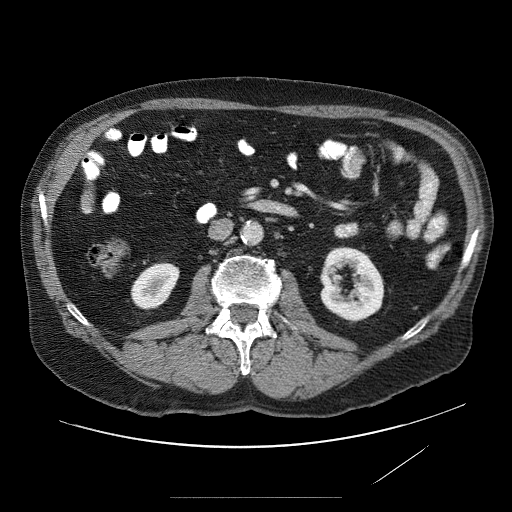
Contrast-enhanced abdominal CT (liver protocol), one axial slice; position 4 of 89 along the scan axis; reconstruction kernel STANDARD; 120 kVp; soft-tissue window (W 400 / L 40 HU); 512 × 512 image matrix, field of view 420 × 420 mm. From the clinical record (not read from this slice): diagnosis: hepatocellular carcinoma (patient treated with transarterial chemoembolisation; whether this scan precedes or follows treatment is not stated here); TNM stage (as recorded): Stage-IVA; Child-Pugh class: A; tumour nodularity: multinodular.
Annotated regions visible in this slice (semi-automatically segmented with operator editing):
- liver parenchyma outside the tumour (the mass and vessels are separate outlines, so this box may not span the whole liver): bounding box <78,160,104,222> (left, top, right, bottom; pixels)
- liver vessels: <95,163,98,167>